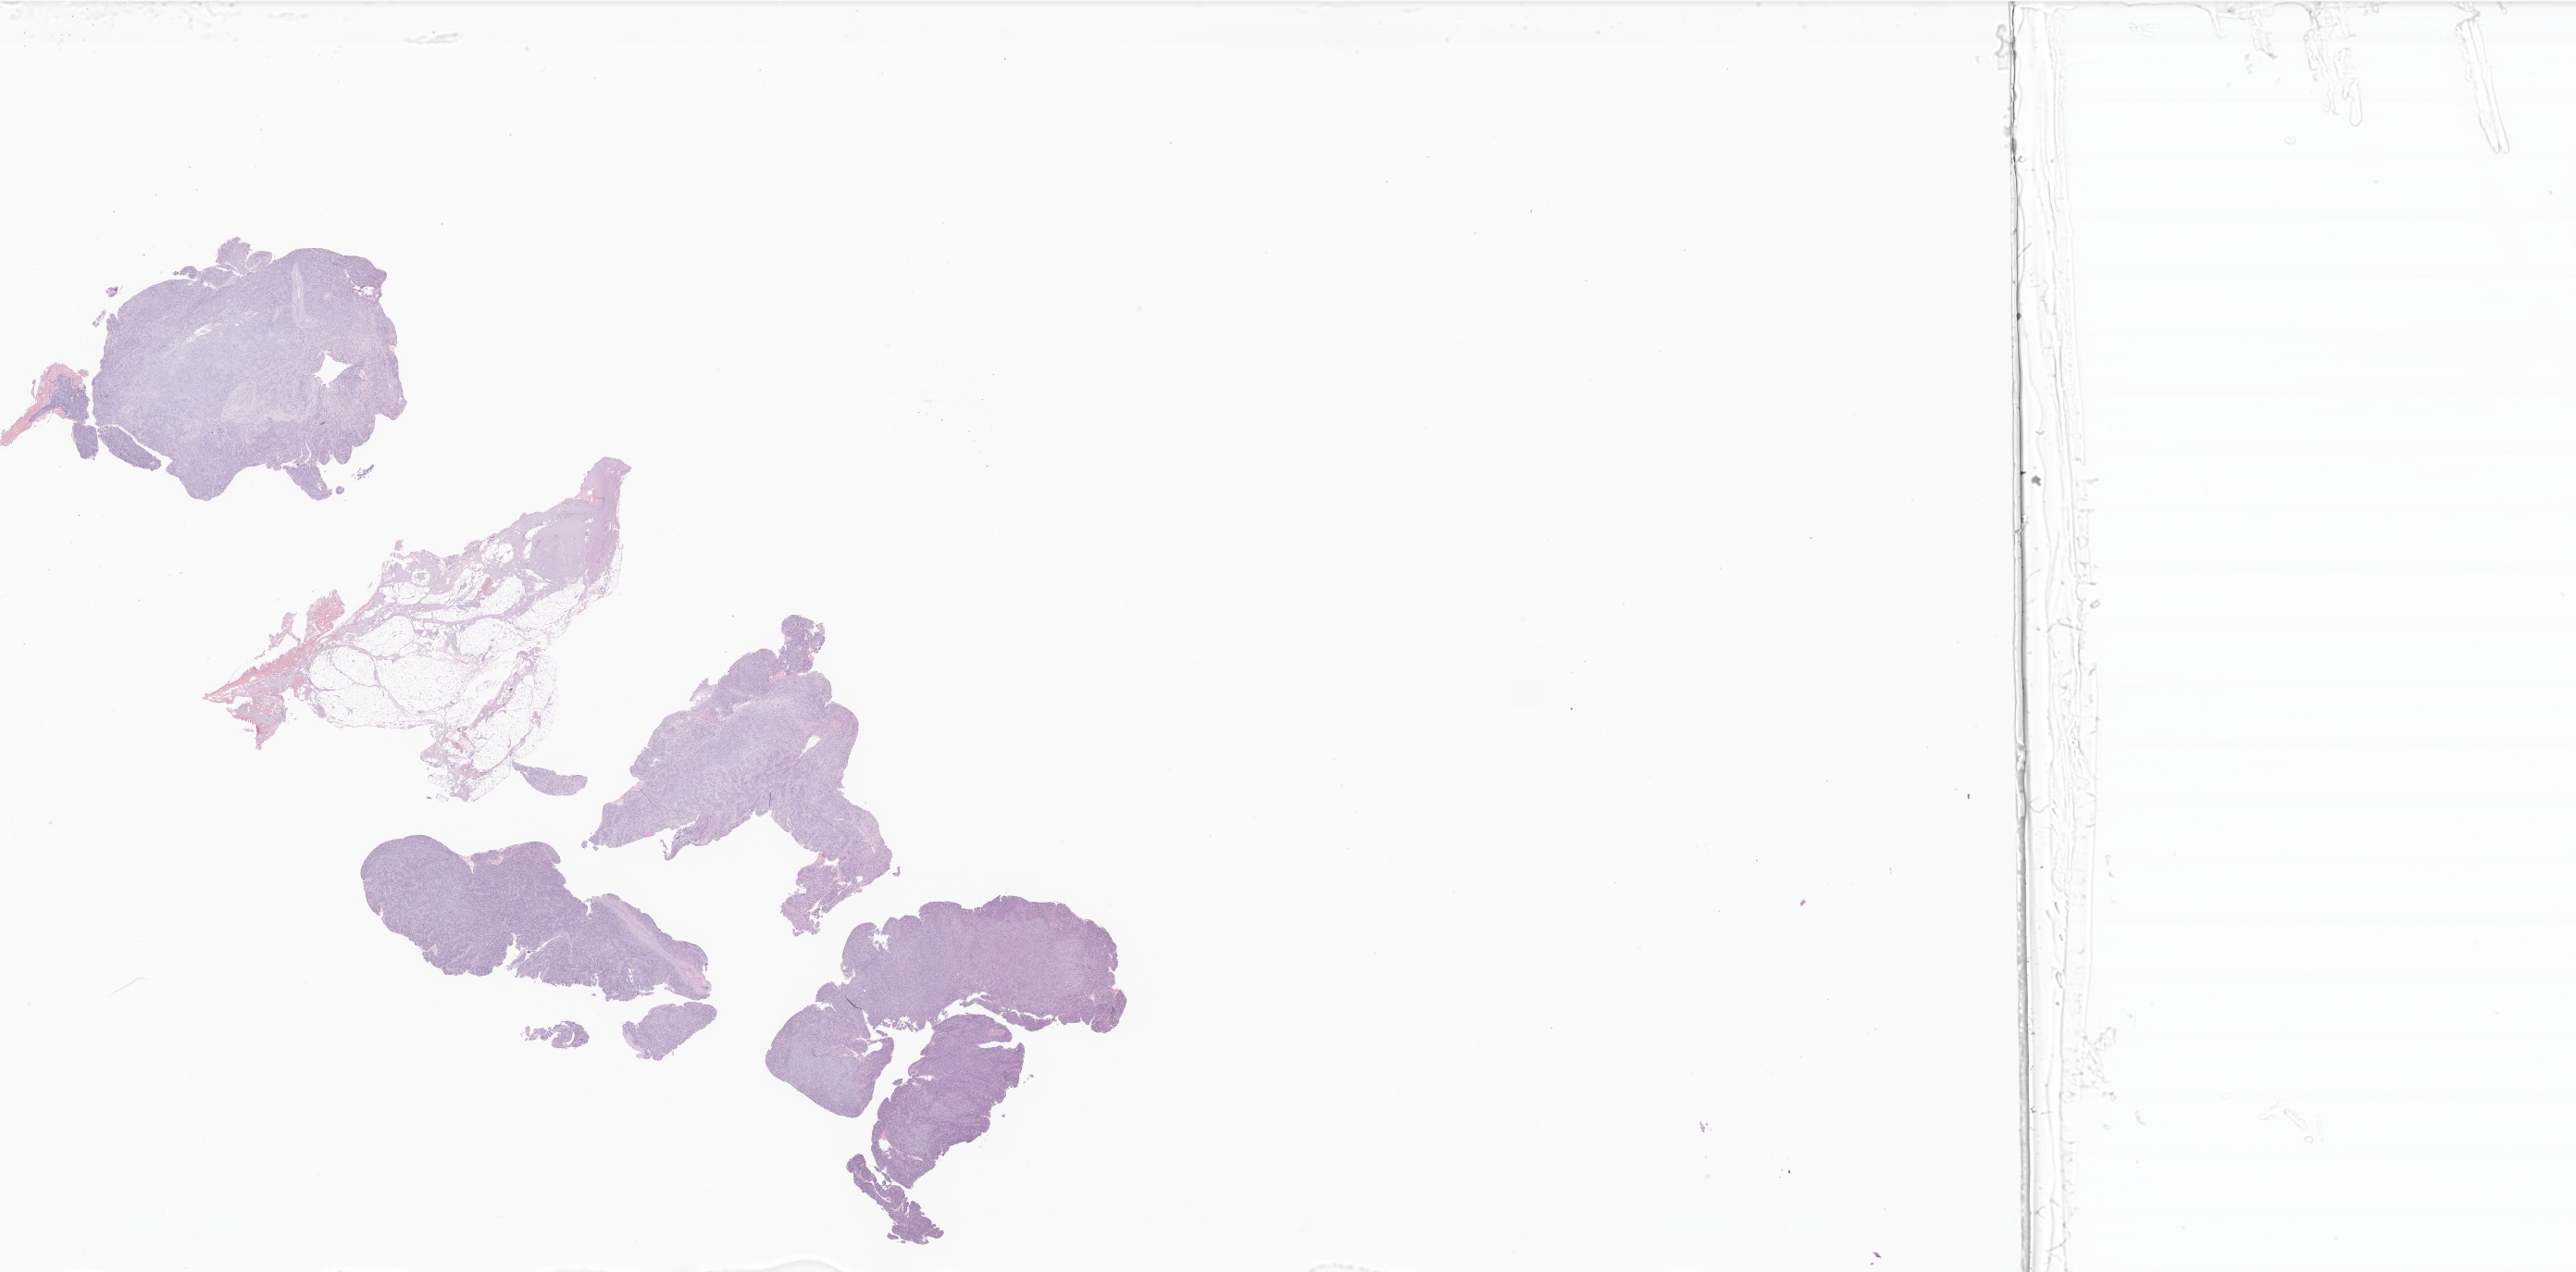
Whole-slide image, haematoxylin and eosin stain of tumor tissue from the pelvis, shown as a low-resolution overview of the whole scanned area (about 46.9 x 23.2 mm); formalin-fixed paraffin-embedded section. Patient: female, age 212 months (17 years 8 months).
Recorded diagnosis: Spindle cell sarcoma.